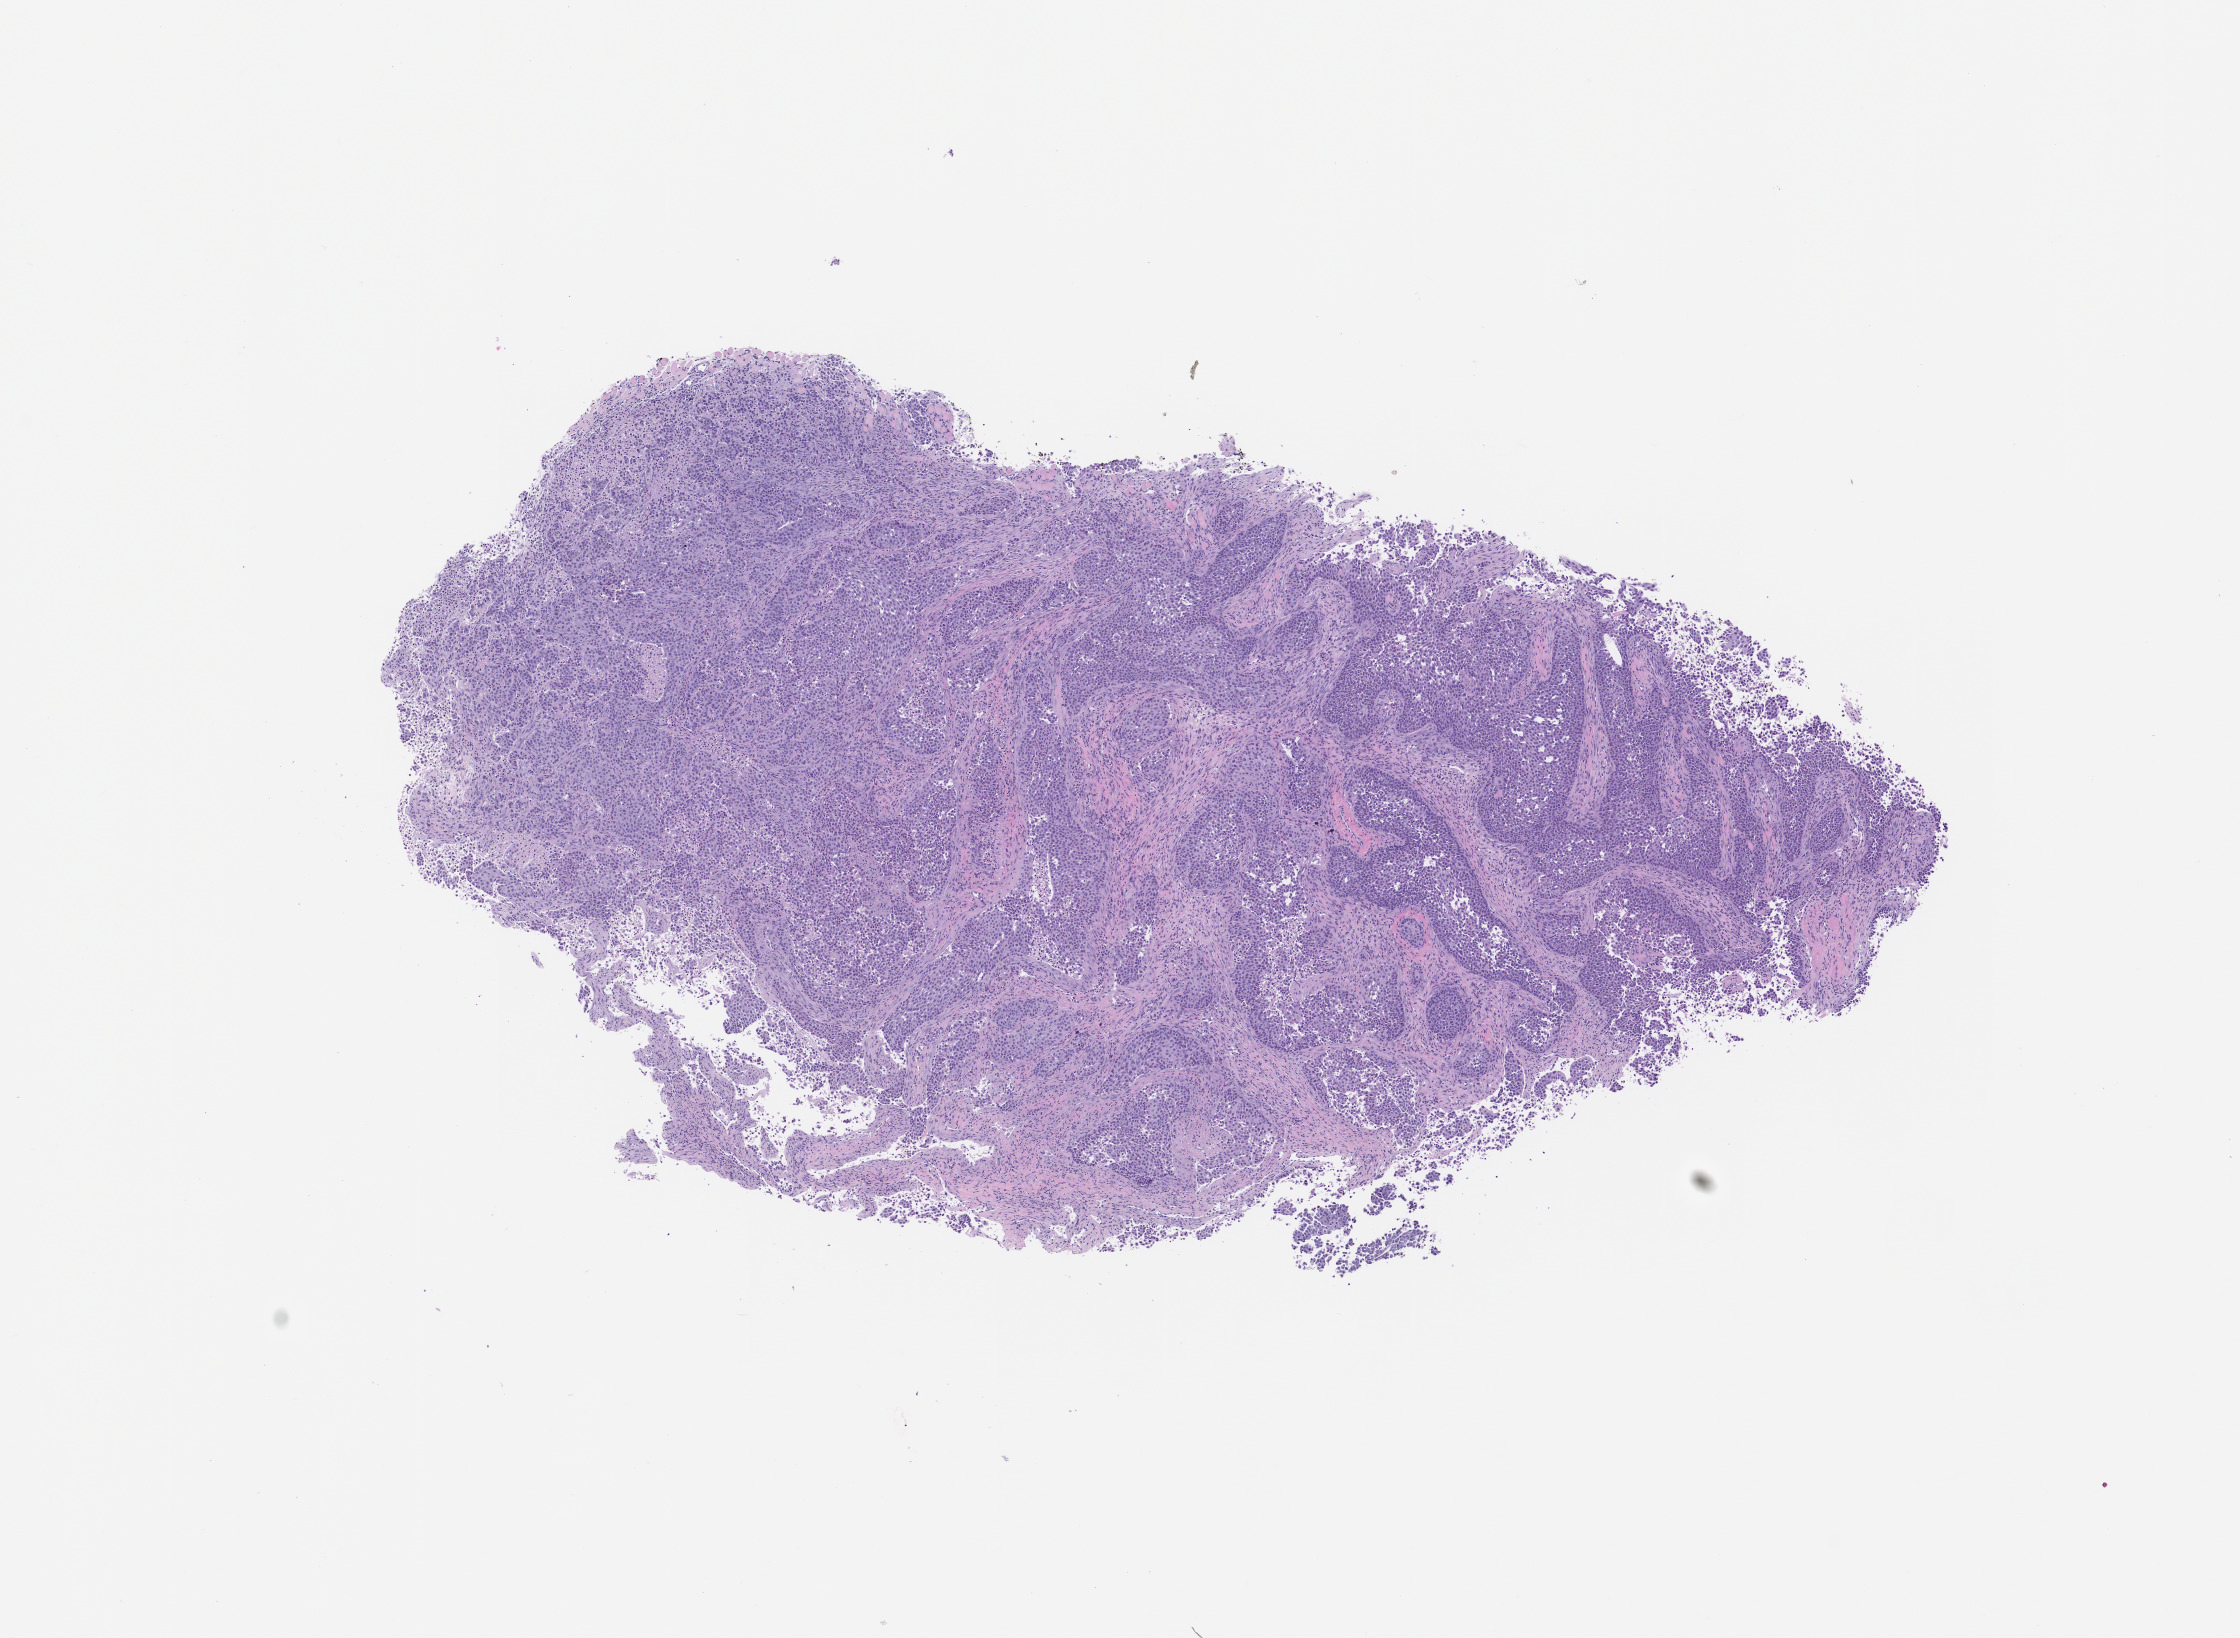
Whole-slide image, hematoxylin and eosin (H&E): patient-derived xenograft (human tumor grown in a mouse), passage 3 — whole scanned area (about 9.0 x 6.6 mm) shown as a low-resolution overview, formalin-fixed, paraffin-embedded (FFPE) tissue, tumor site category: bladder.
- originating patient diagnosis: Transitional Cell Carcinoma